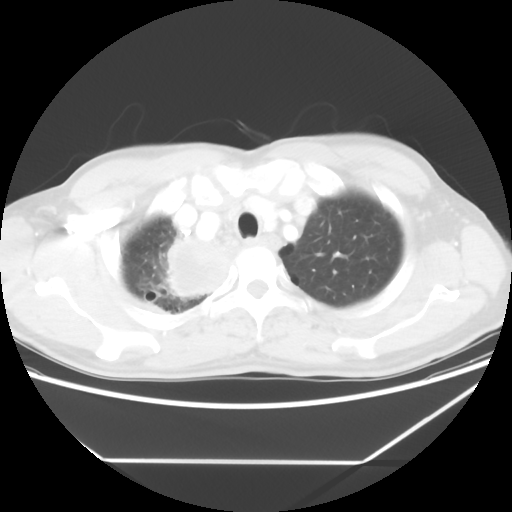
Chest CT, one axial slice. Slice 52 of 60 in the series (ordered by position). Lung window (W 1500 / L -600 HU). 5 mm slice thickness. 512 × 512 image matrix. Patient: male, 58 years. Case-level facts recorded for this patient, not image findings: clinical TNM (as recorded): T2 N2 M0.
Annotated regions visible in this slice (rectangle marked by the reading radiologist):
- lung tumour (recorded histology: squamous cell carcinoma): bounding box [x1, y1, x2, y2] px = [154, 229, 244, 305]